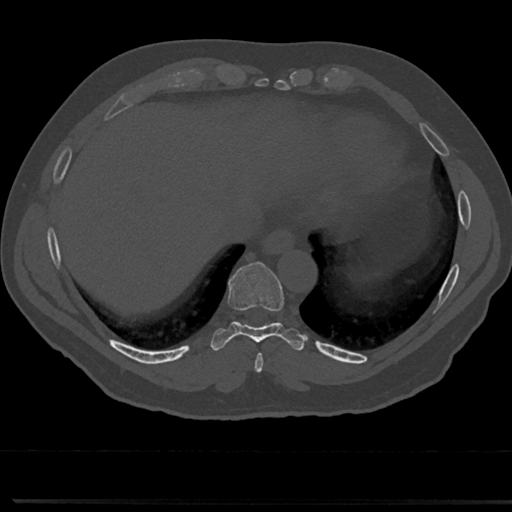
CT including the spine, one axial slice. Slice 303 of 817 in the series (ordered by position). Bone window (W 1800 / L 400 HU). 0.5 mm slice thickness. 512 × 512 image matrix, field of view 355 × 355 mm. Male patient, age 61 years. Case-level facts recorded for this patient, not image findings: primary cancer: prostate.
Outlined on this slice (semi-automatically segmented with operator editing):
- T8 vertebra: box from (x=234, y=306) to (x=285, y=356) px
- T9 vertebra: (x=232, y=266)–(x=283, y=330)